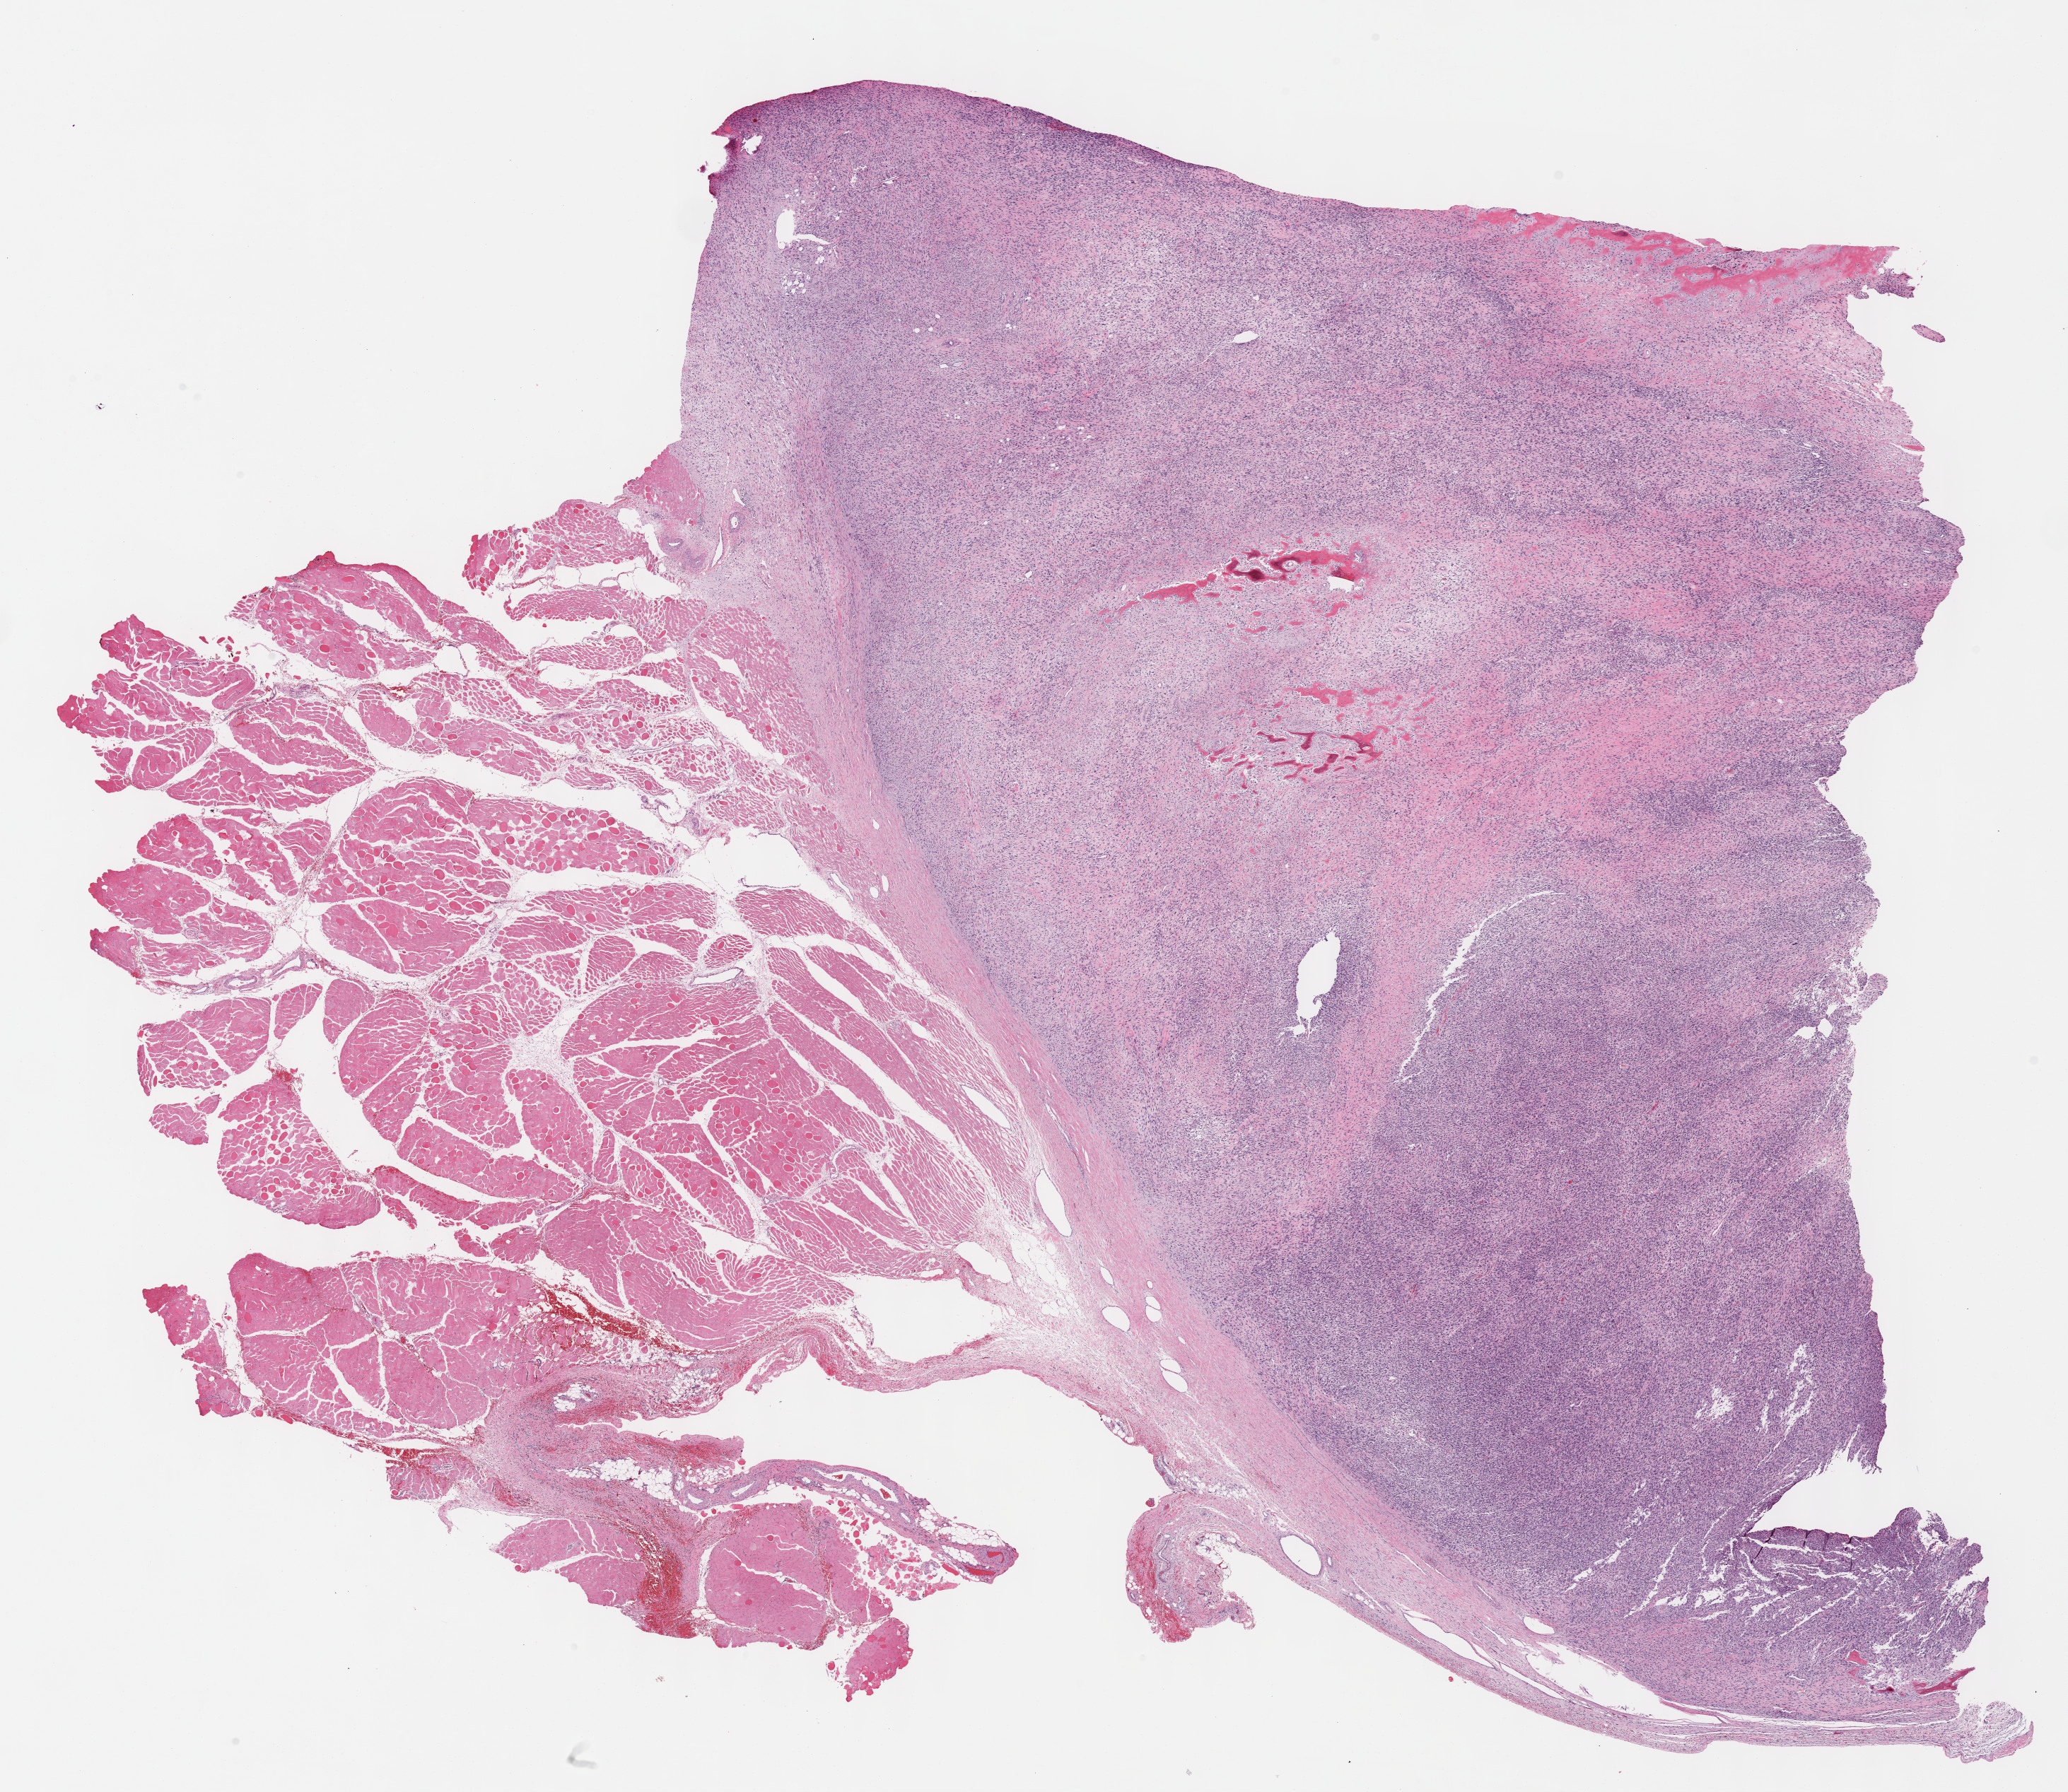
Whole-slide histology image, H&E-stained — a low-resolution overview of the entire scanned area, about 23.6 x 20.5 mm (slide scanned at 40x); FFPE section; primary tumour sample from the retroperitoneum and peritoneum. Patient: male, age at initial diagnosis 72 years.
- diagnosis: Sarcoma, NOS (retroperitoneum)